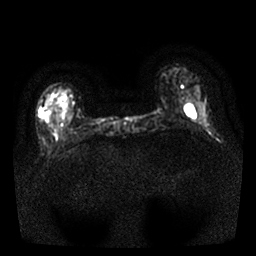
Breast MRI, one axial slice; position 6 of 25 along the scan axis; diffusion-weighted series; image 2 of 4 stored at this slice position (different b-values; order by instance number); 1.5 T; 4 mm slice thickness; 256 × 256 image matrix. Female patient.
Structures marked on this image (expert manual segmentation):
- tumour on diffusion-weighted imaging: bounding box (x1, y1, x2, y2) in pixels: (38, 107, 48, 122)